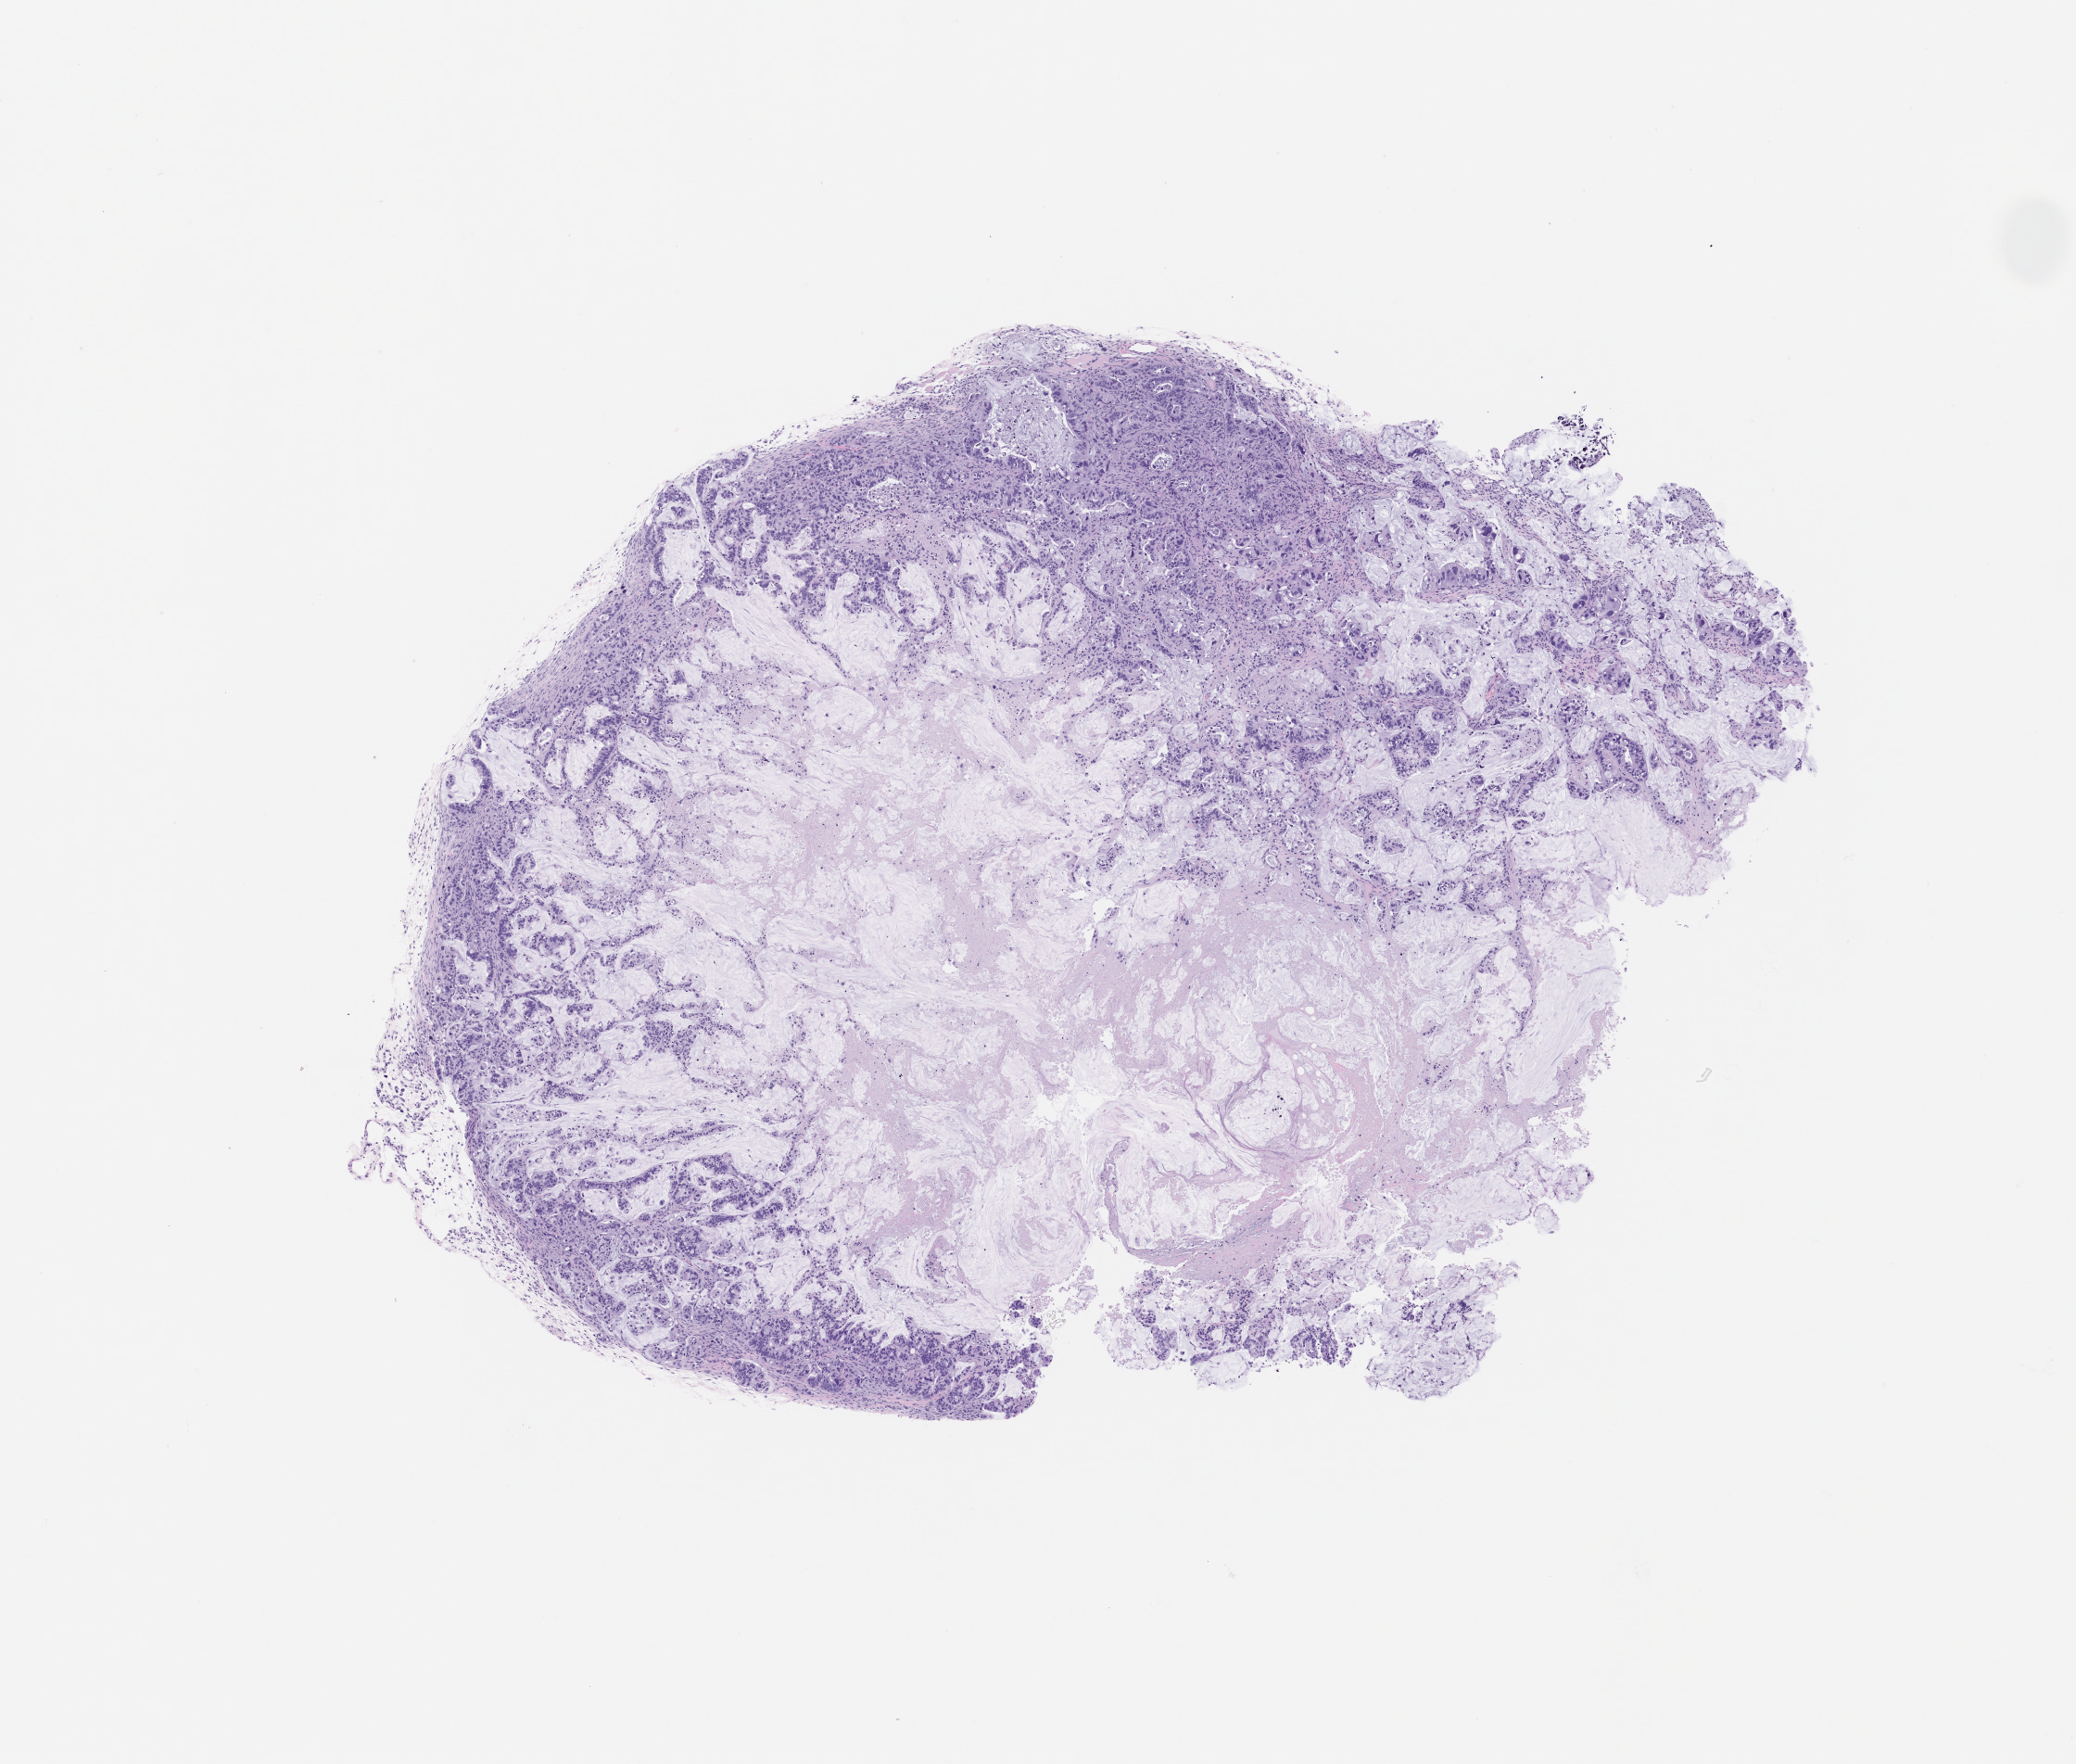
Whole-slide image, H&E: patient-derived xenograft (human tumor grown in a mouse), passage 2 — a low-resolution overview of the entire scanned area, about 9.0 x 7.6 mm; formalin-fixed, paraffin-embedded (FFPE) tissue; originating tumor site category: pancreas.
* originating patient diagnosis: Pancreatic Adenocarcinoma